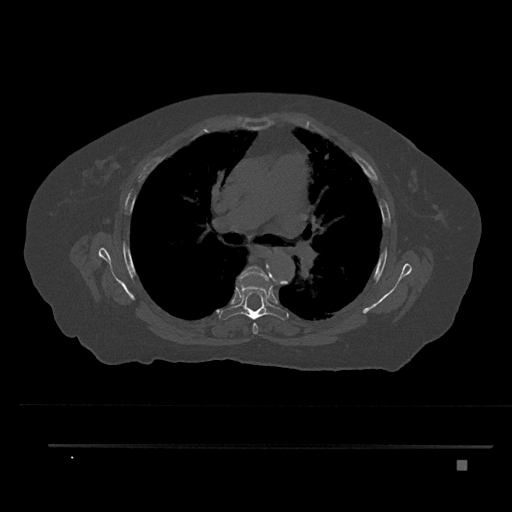
CT including the spine, one axial slice. Slice 538 of 797 in the series (ordered by position). Bone window (W 1800 / L 400 HU). 0.5 mm slice thickness. 512 × 512 image matrix. Patient: female, 76 years. From the clinical record (not read from this slice): primary cancer: lung; vertebrae with lytic lesions (as recorded): T11, L3.
Structures marked on this image (semi-automatic segmentation, software-assisted and operator-edited):
- T5 vertebra: box from (x=236, y=266) to (x=269, y=334) px
- T6 vertebra: (x=219, y=277)–(x=289, y=321)